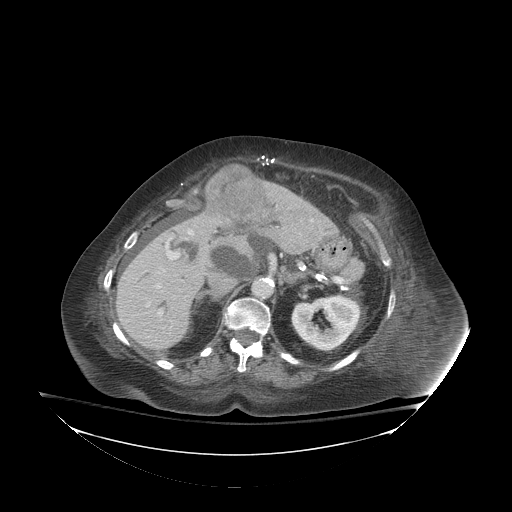
Contrast-enhanced abdominal CT (liver protocol), one axial slice; position 51 of 81 along the scan axis; 140 kVp; soft-tissue window (W 400 / L 40 HU); 512 × 512 image matrix, field of view 500 × 500 mm. Case-level facts recorded for this patient, not image findings: diagnosis: hepatocellular carcinoma (patient treated with transarterial chemoembolisation; whether this scan precedes or follows treatment is not stated here); TNM stage (as recorded): Stage-I.
Outlined on this slice (semi-automatically segmented with operator editing):
- liver parenchyma outside the tumour (the mass and vessels are separate outlines, so this box may not span the whole liver): bounding box <116,182,324,350> (left, top, right, bottom; pixels)
- mass: <207,164,270,224>
- liver vessels: <156,230,193,314>